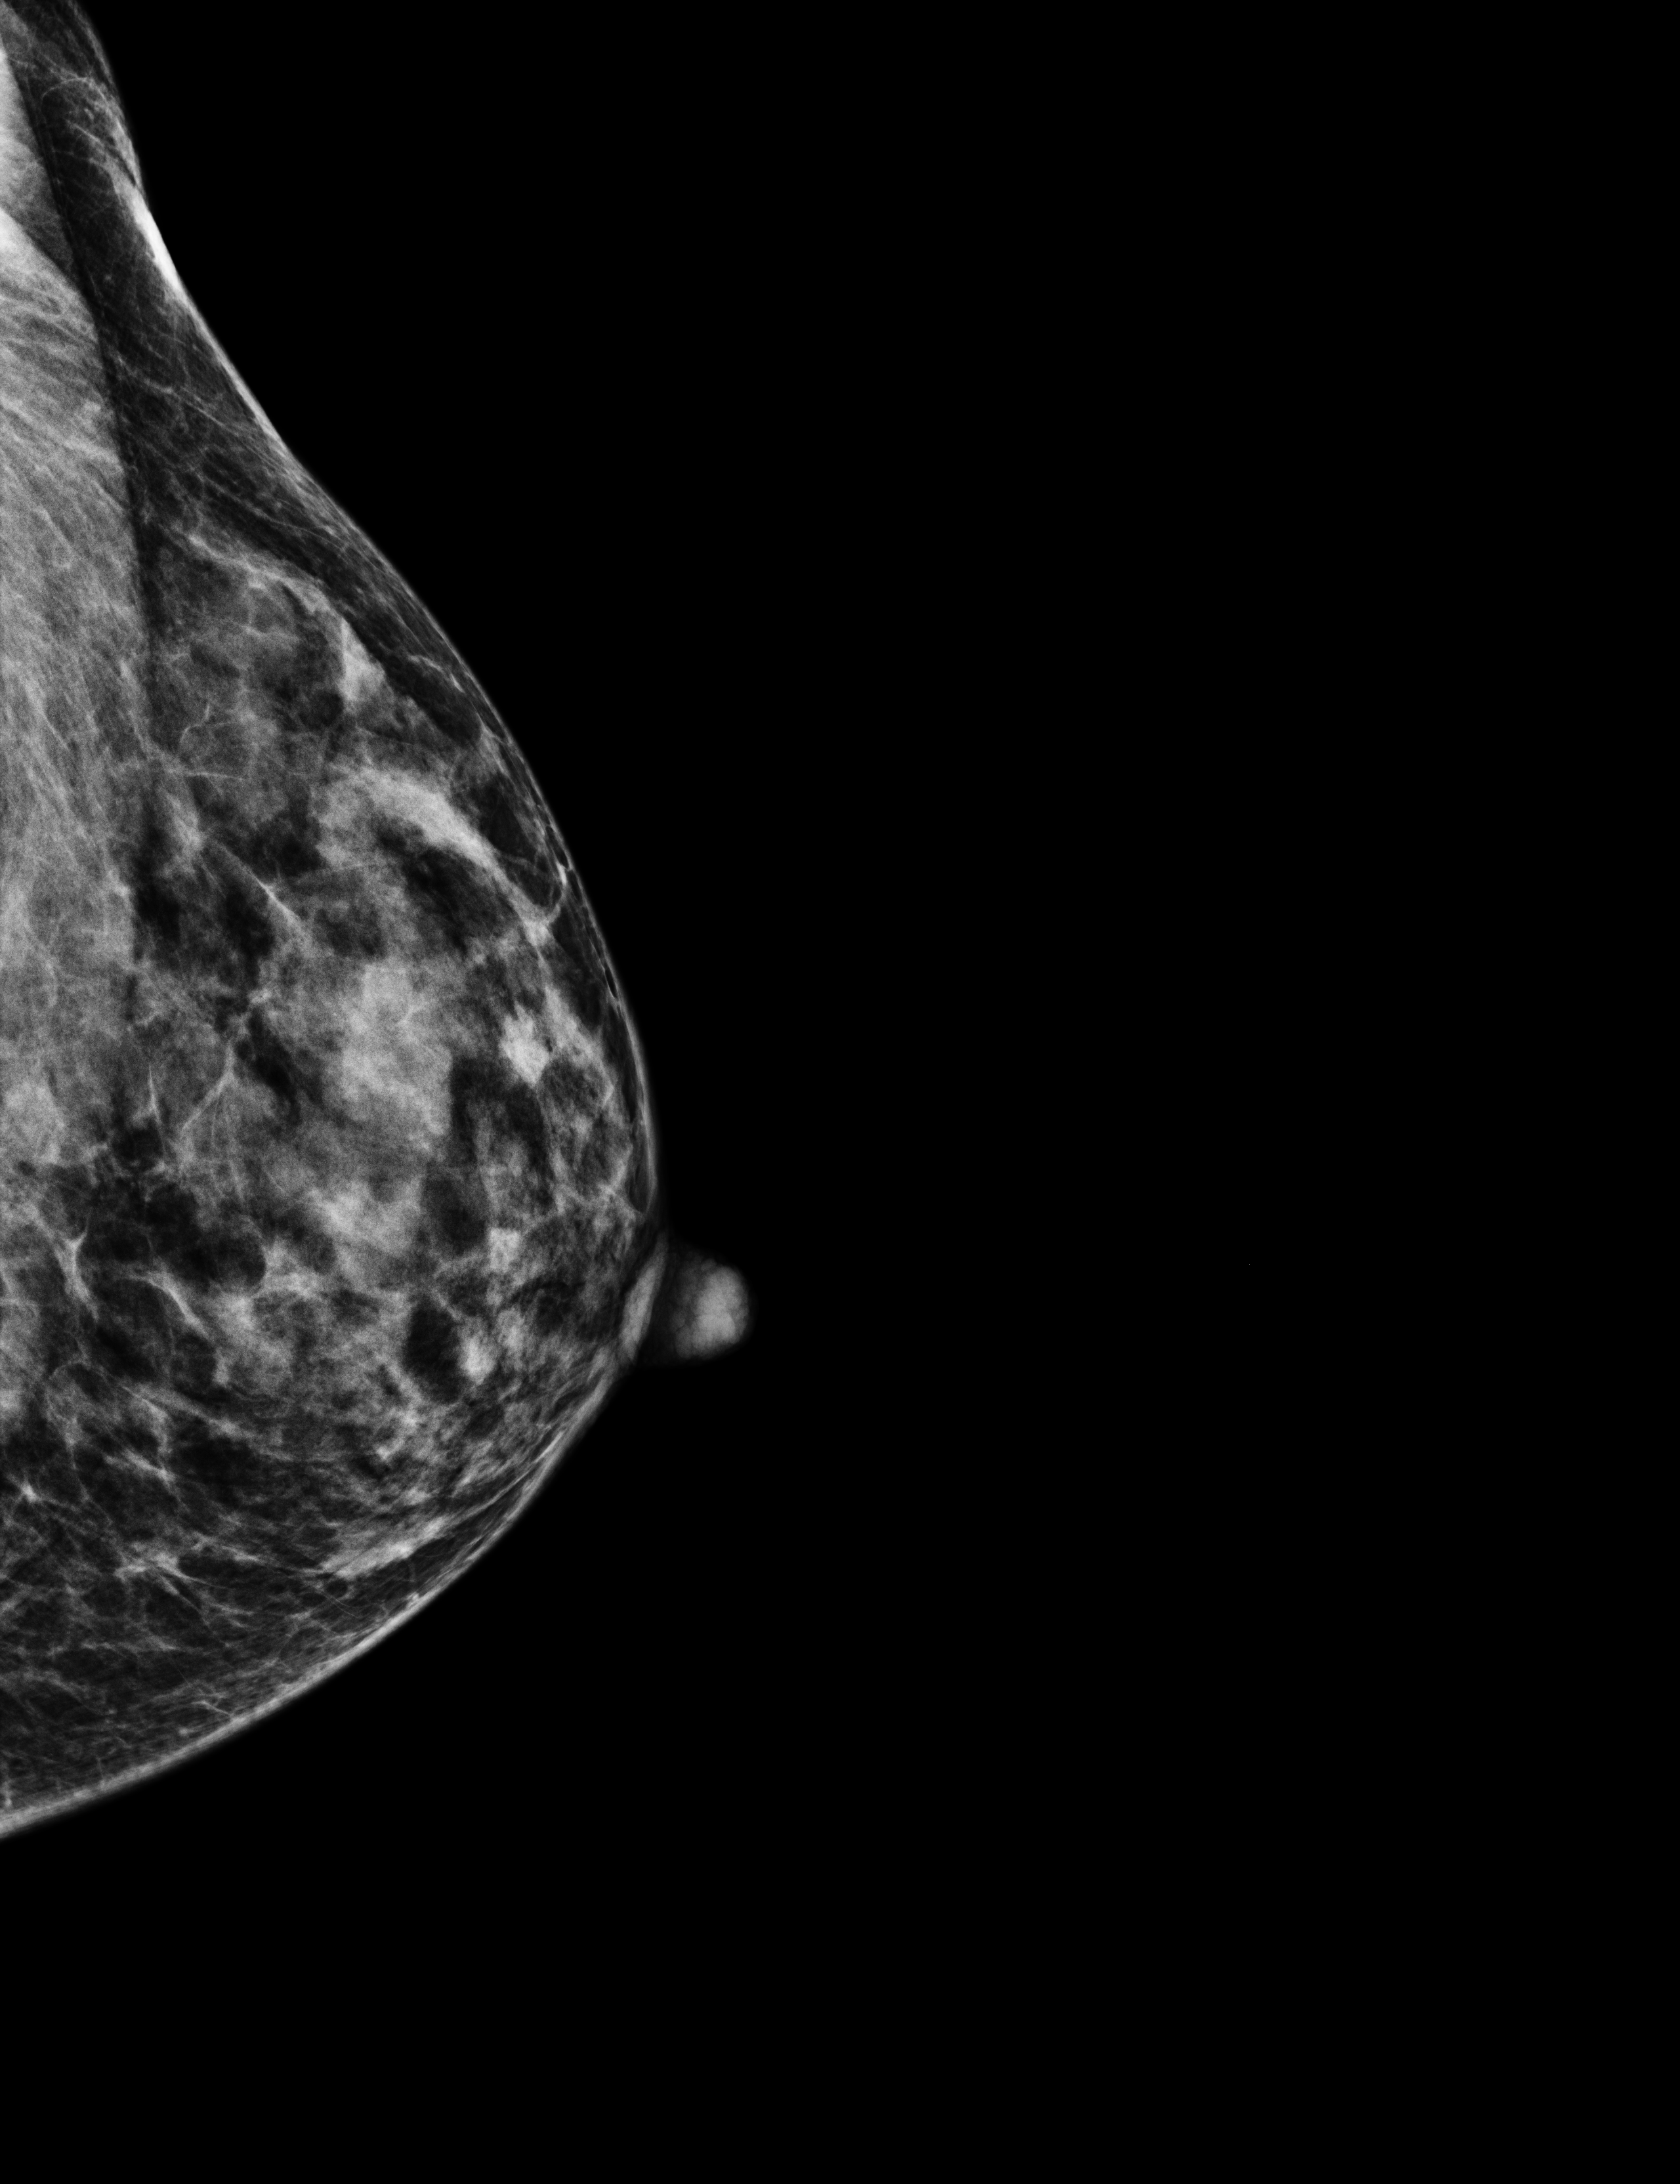
Screening examination, system: Selenia Dimensions. Female patient, age 54 years.
Image type: full-field digital mammogram. Breast: left. Projection: laterally exaggerated craniocaudal (XCCL) view.